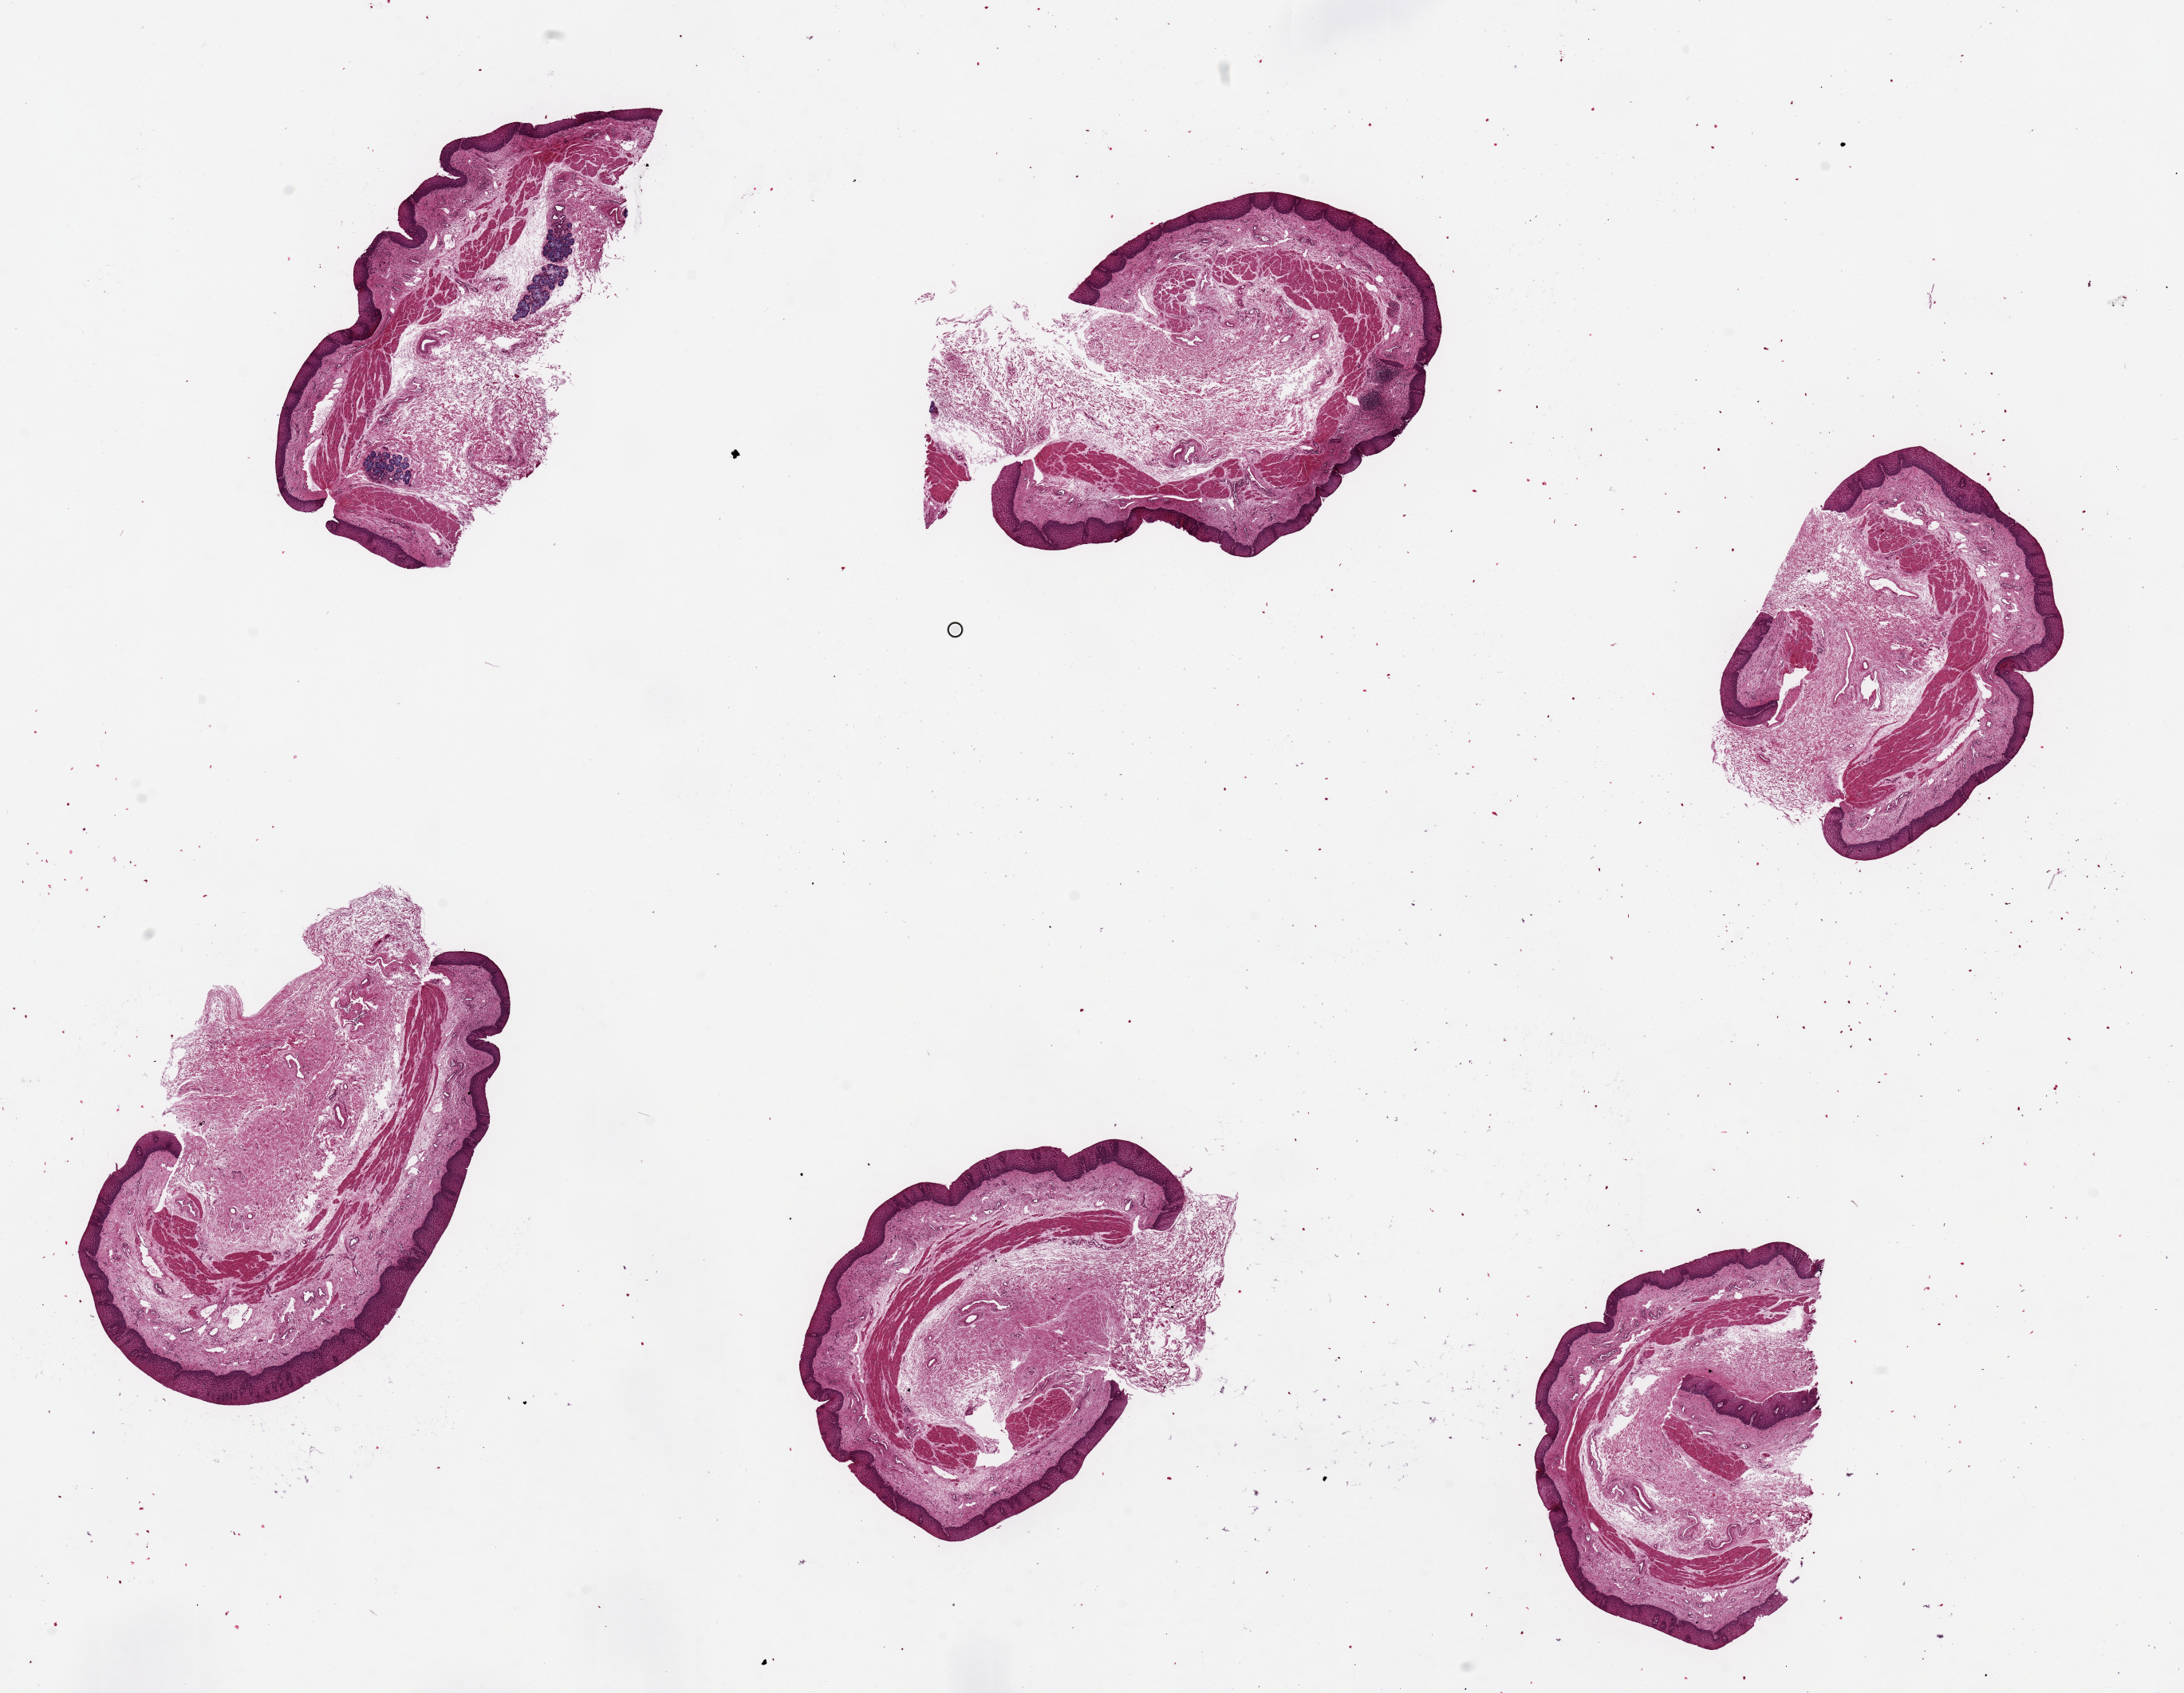
Hematoxylin and eosin (H&E) whole-slide image, brightfield — a low-resolution overview of the entire scanned area, about 21.7 x 16.8 mm; PAXgene-fixed, paraffin-embedded tissue; section of esophageal mucous membrane (target tissue); tissue donor sample. Donor: female.
Review note (as recorded): 6 pieces, ~5x2.5mm, squamous mucosa is ~5-10% thickness.